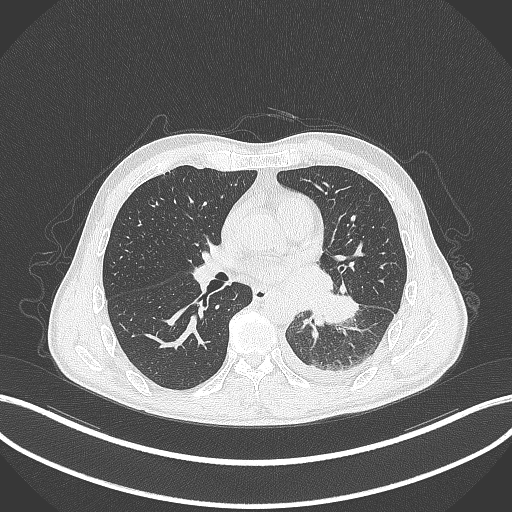
Chest CT, one axial slice; slice 159 of 295 in the series (ordered by position); reconstruction kernel B70f; lung window (W 1500 / L -600 HU); 1 mm slice thickness; 512 × 512 image matrix. Patient: male, 47 years. Case-level facts recorded for this patient, not image findings: clinical TNM (as recorded): T3 N1 M1c; histopathological grade: G3.
Annotated regions visible in this slice (bounding box drawn by a radiologist):
- lung tumour (recorded histology: small cell carcinoma): bounding box <306,286,361,329> (left, top, right, bottom; pixels)